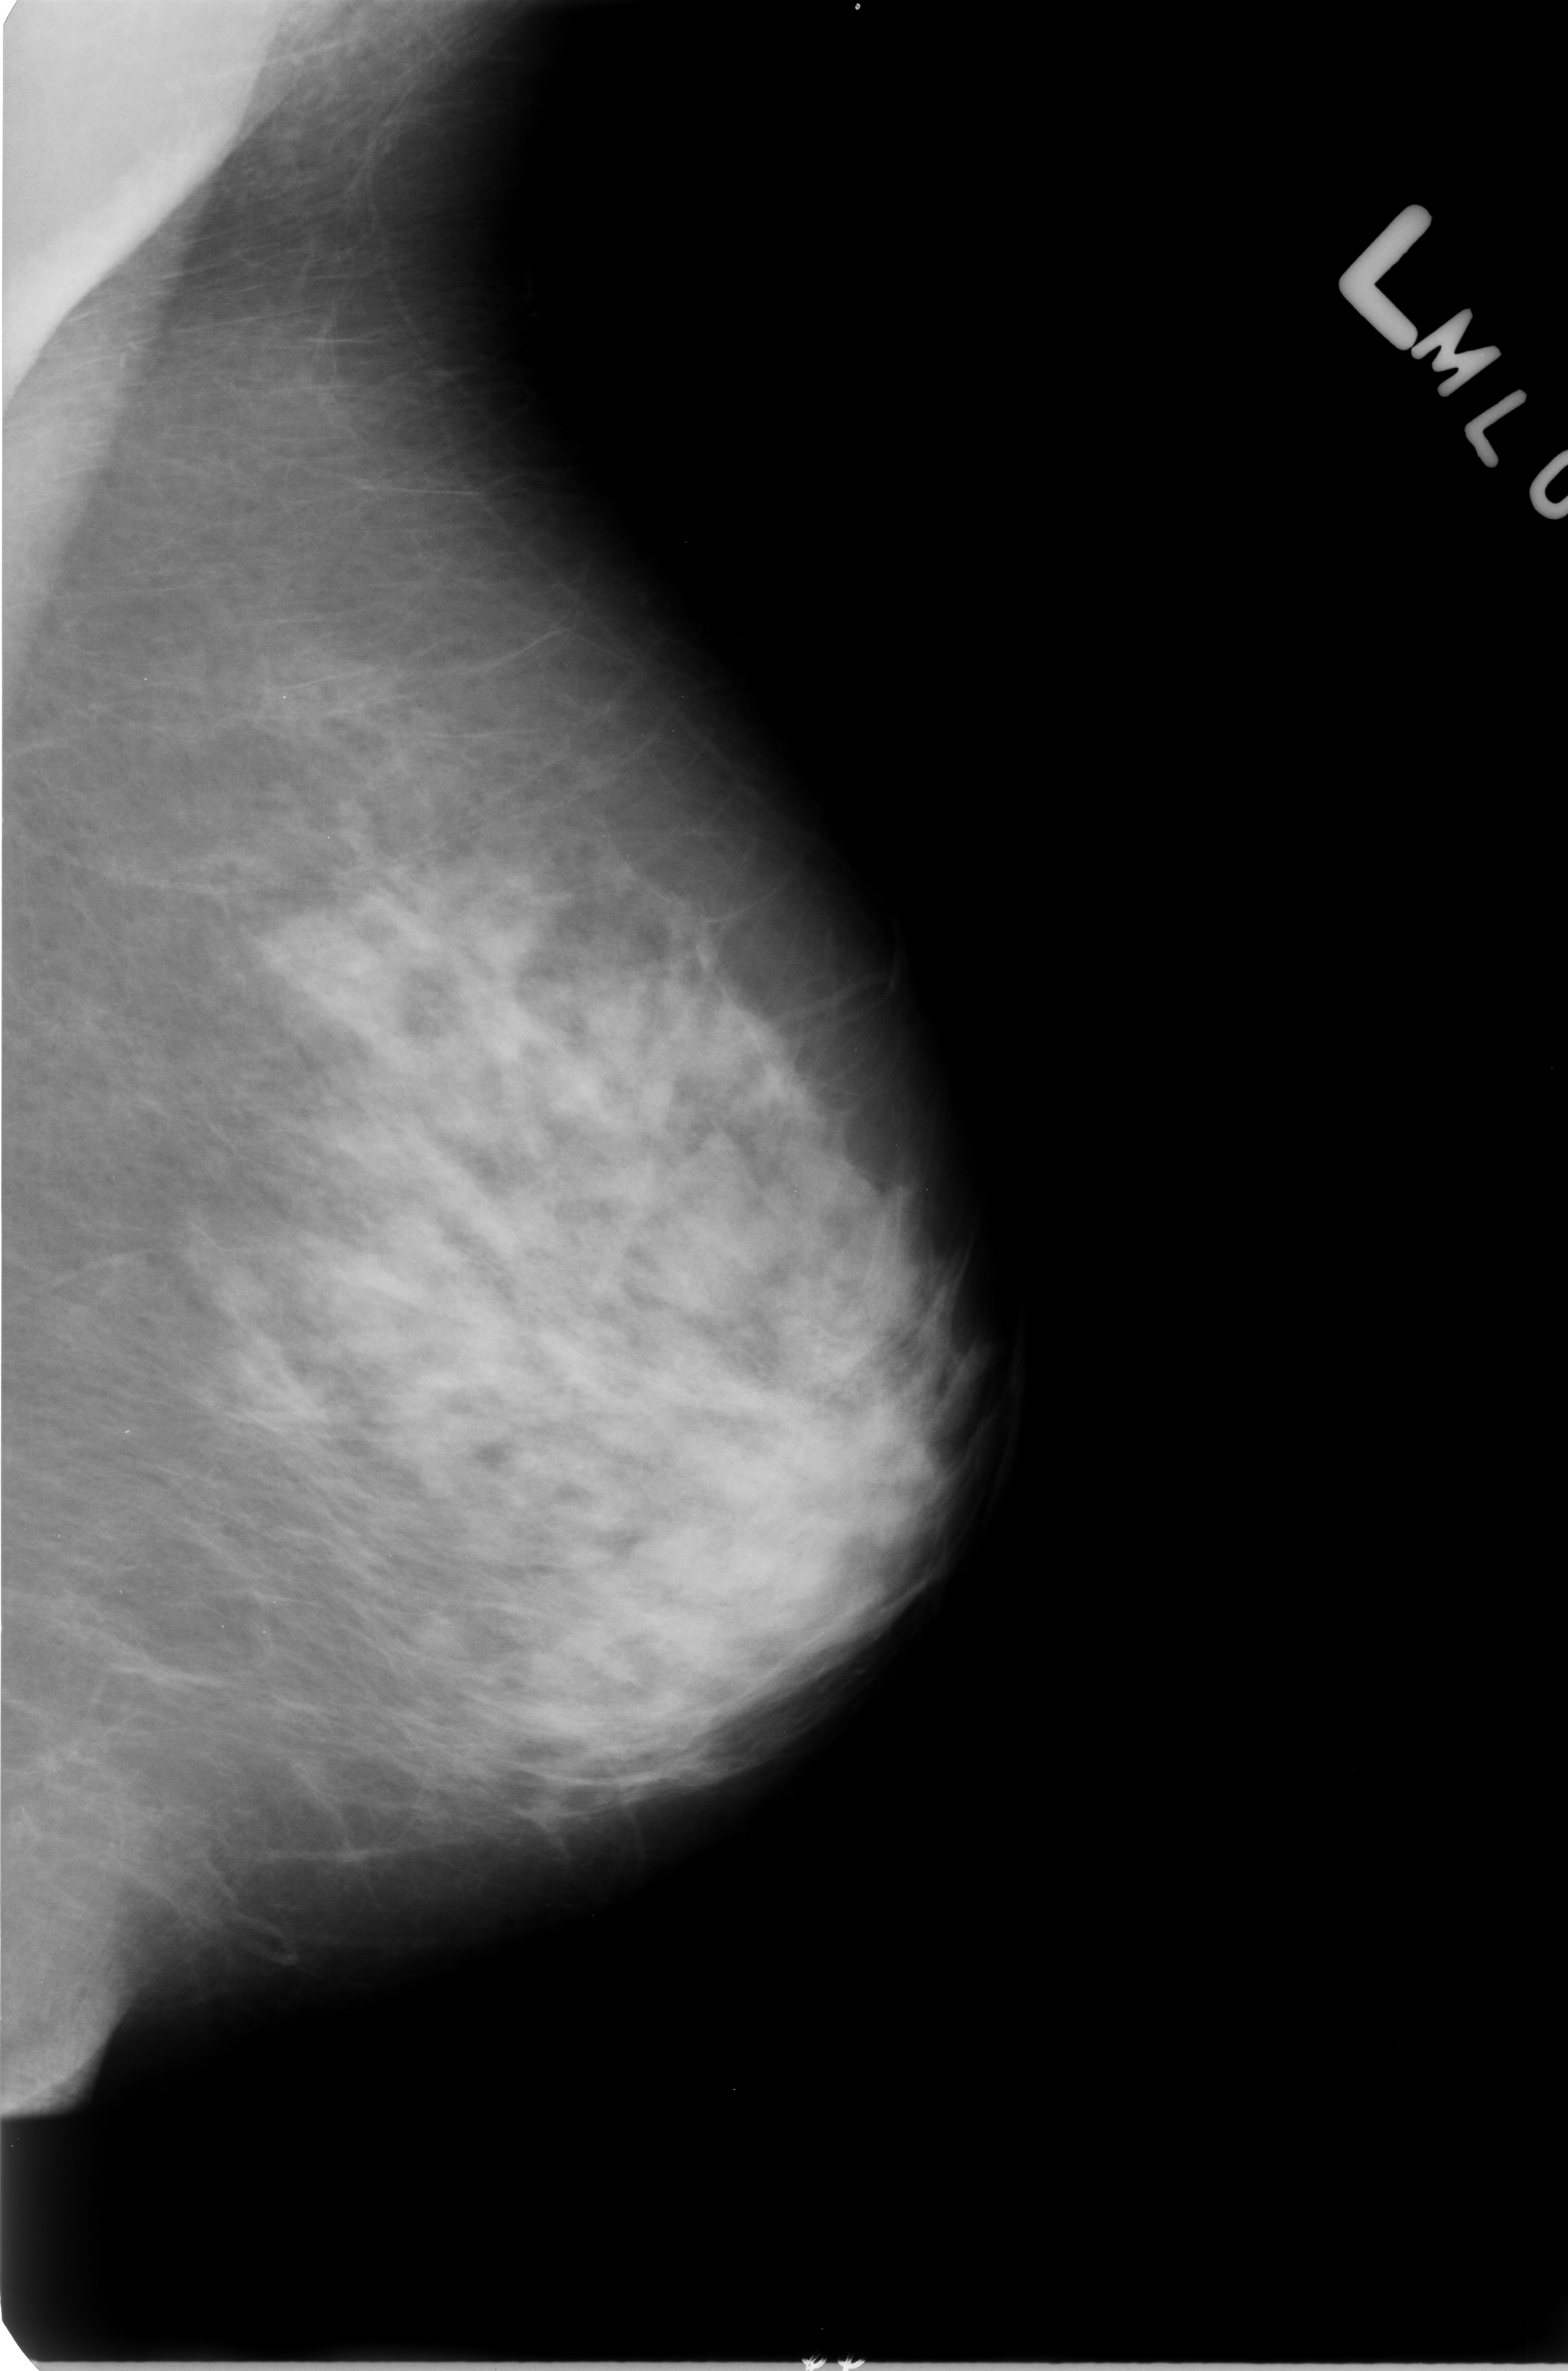
Scanned film-screen mammogram; left breast; MLO view; BI-RADS breast density category 3 (scale 1–4); 1568 × 2371 image matrix.
Expert-marked regions of interest on this film, with their recorded descriptors:
- calcifications, morphology vascular; BI-RADS assessment category 2; outcome (as recorded, no biopsy): benign without callback (not worked up further): bounding box <0,802,472,947> (left, top, right, bottom; pixels)